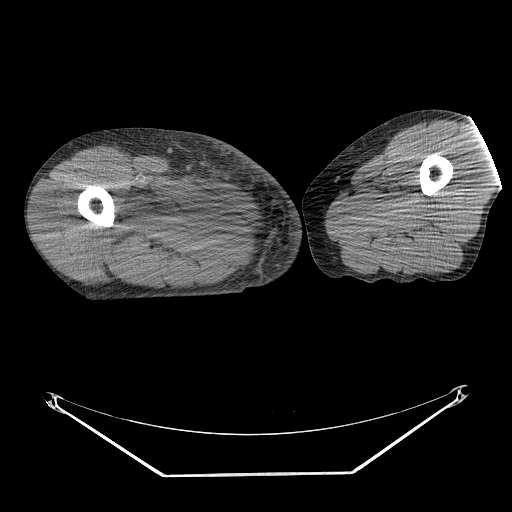
CT of an extremity soft-tissue mass (from a PET/CT study), one axial slice. Position 241 of 311 along the scan axis. Reconstruction kernel STANDARD. 140 kVp. Soft-tissue window (W 400 / L 40 HU). 512 × 512 image matrix, field of view 500 × 500 mm. Male patient. From the clinical record (not read from this slice): histological type: undifferentiated - pleiomorphic; grade: high; site of the primary tumour: right thigh.
Structures marked on this image (expert contour drawn on MRI and transferred to this co-registered scan by the dataset authors):
- gross tumour volume including surrounding oedema: bounding box <128,176,213,238> (left, top, right, bottom; pixels)
- gross tumour volume (mass): <174,192,213,225>